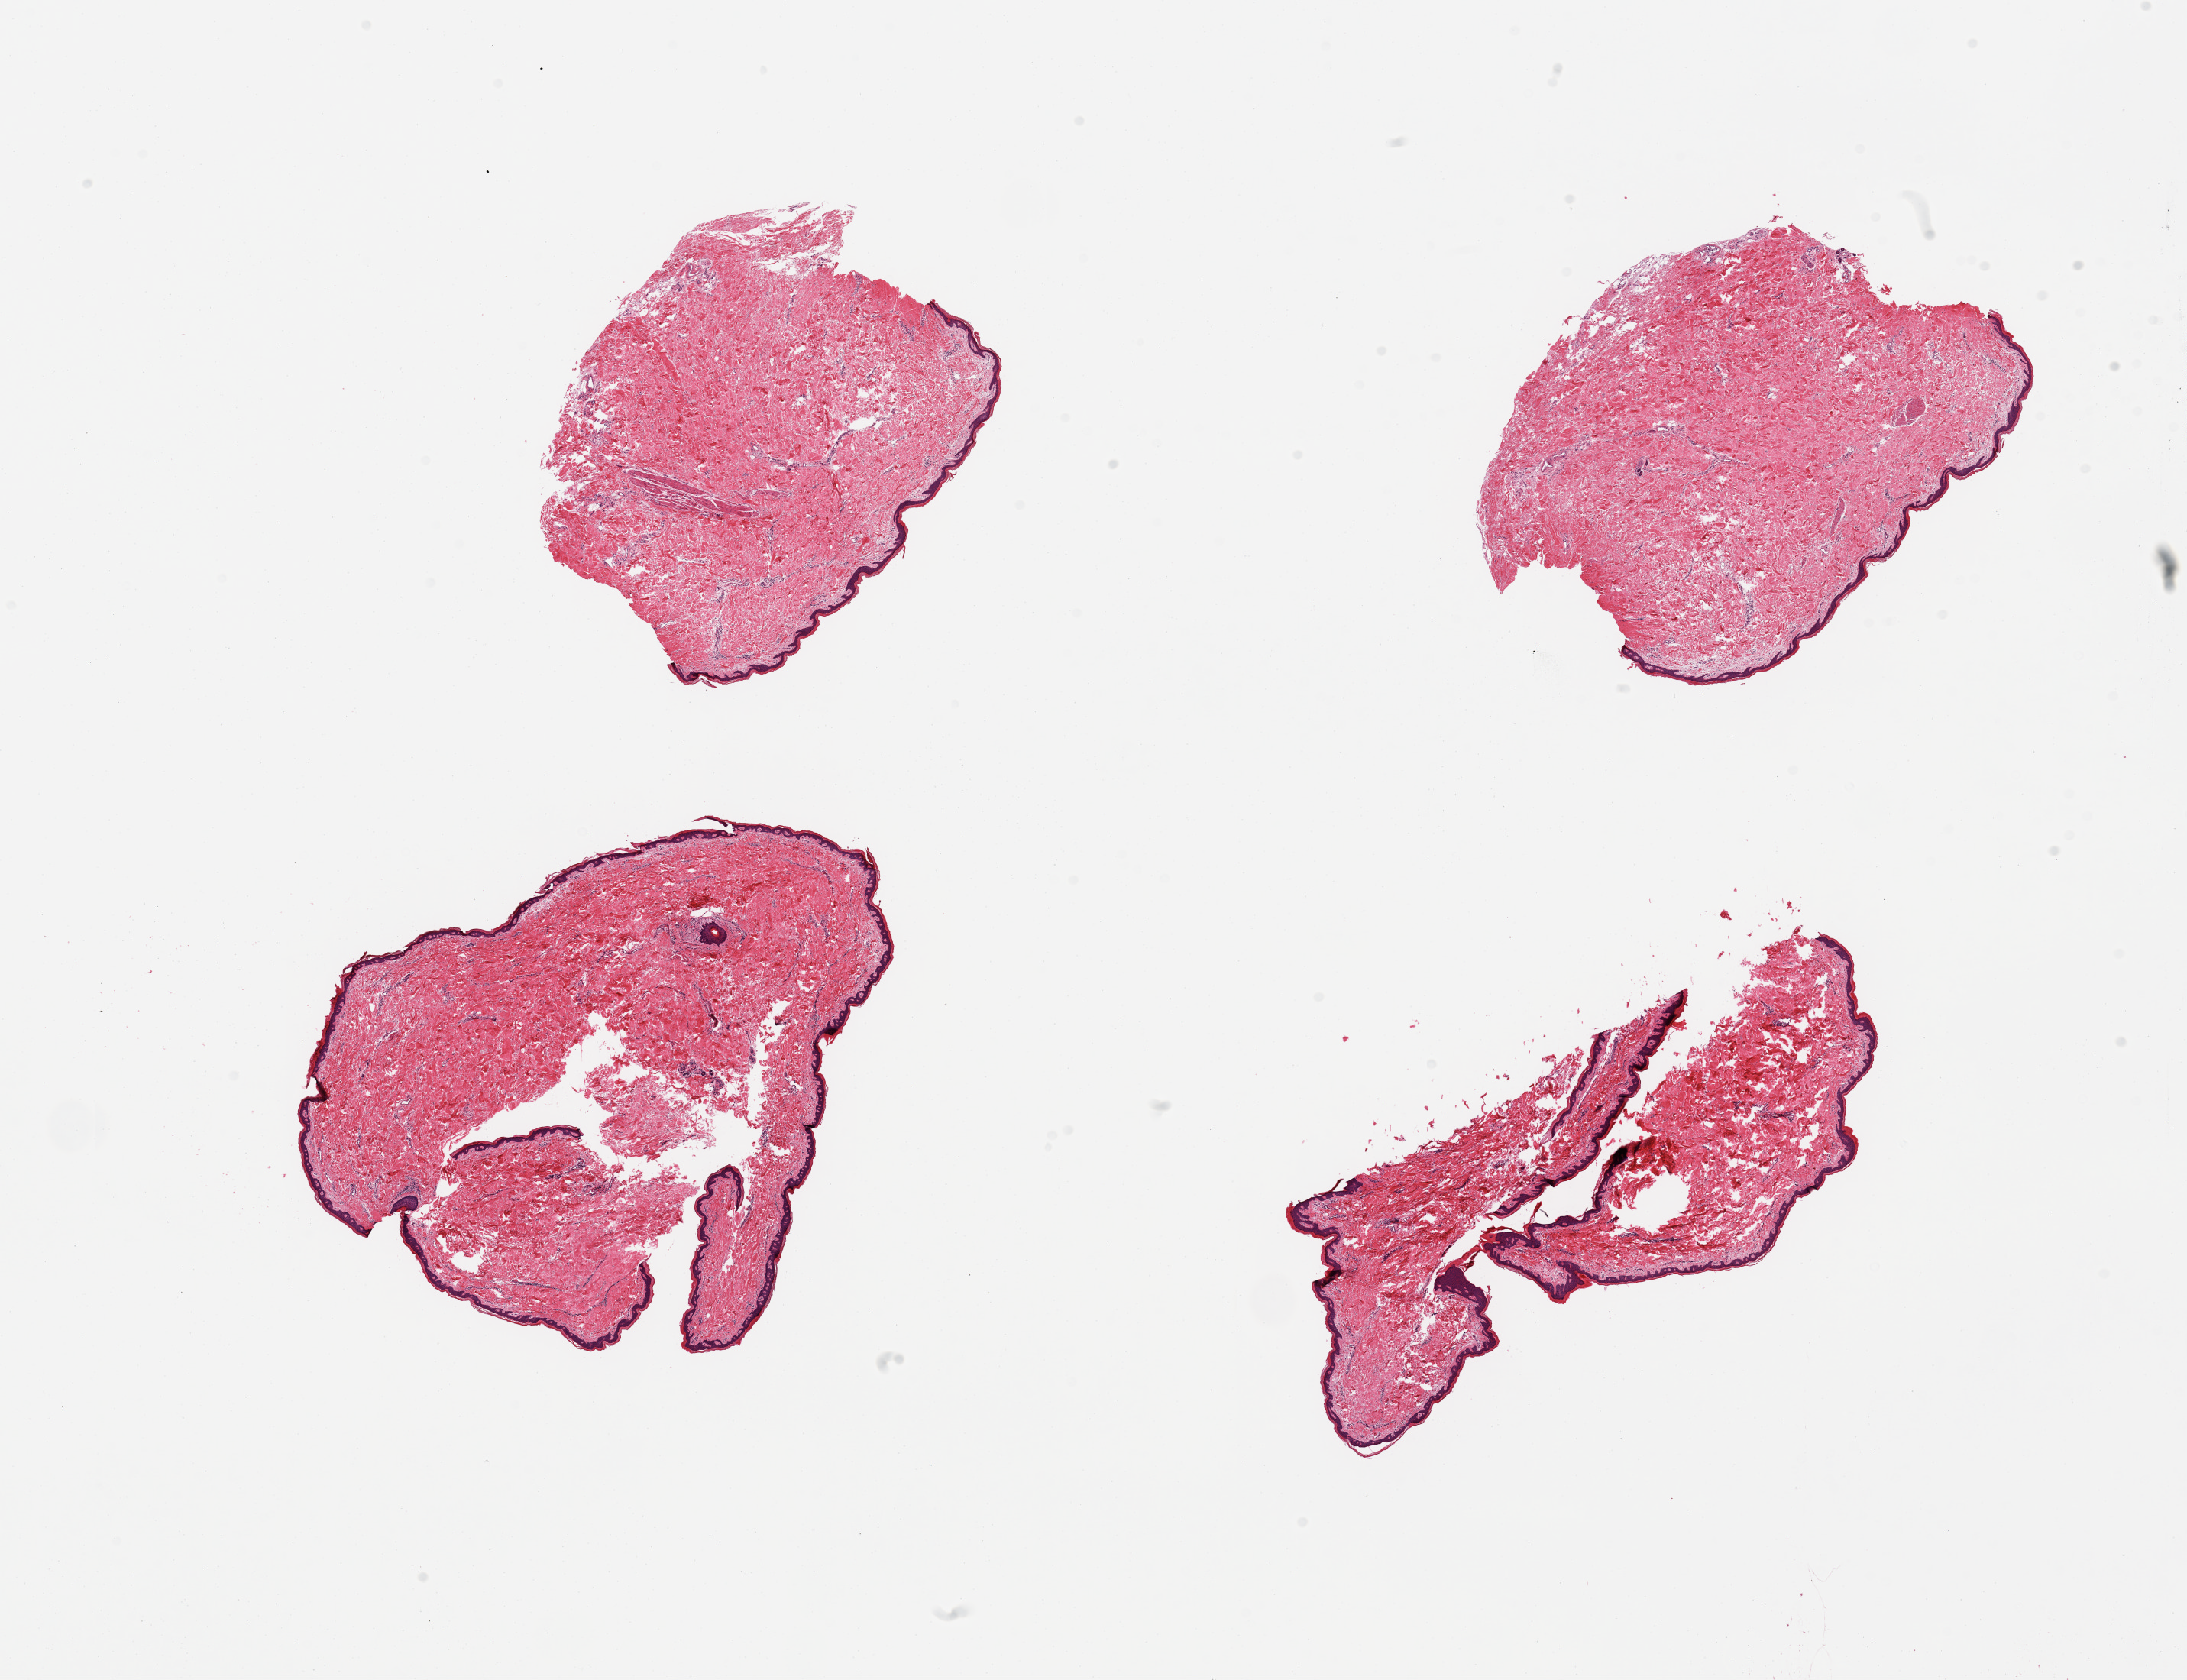
Whole-slide image, H&E stain, shown as a low-resolution overview of the whole scanned area (about 22.6 x 17.4 mm, slide scanned at 20x). PAXgene-fixed paraffin-embedded (PFPE) section. Section of skin of suprapubic region (target tissue). Donor tissue sample. Donor: male.
* reviewer comment on this tissue sample: 4 pieces, minimeal dermal fat, squamous epithelium is ~35-40 microns